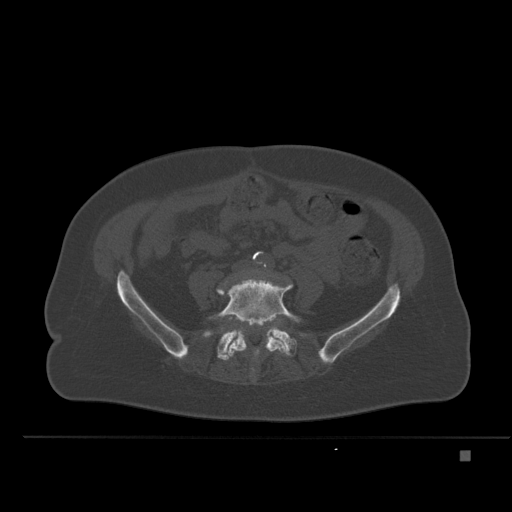
CT including the spine, one axial slice. Position 160 of 477 along the scan axis. Bone window (W 1800 / L 400 HU). 1.5 mm slice thickness. 512 × 512 image matrix, field of view 422 × 422 mm. Female patient, age 74 years. From the clinical record (not read from this slice): primary cancer: colon.
Annotated regions visible in this slice (semi-automatically segmented with operator editing):
- L4 vertebra: bounding box (x1, y1, x2, y2) in pixels: (217, 289, 222, 293)
- L5 vertebra: (209, 278, 301, 360)